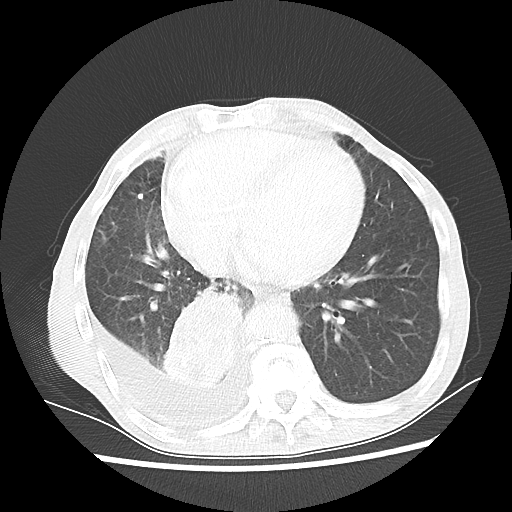
Chest CT, one axial slice; slice 22 of 60 in the series (ordered by position); reconstruction kernel LUNG; lung window (W 1500 / L -600 HU); 5 mm slice thickness; 512 × 512 image matrix. Male patient, age 76 years. From the clinical record (not read from this slice): clinical TNM (as recorded): T3 N3 M1a.
Annotated regions visible in this slice (rectangle marked by the reading radiologist):
- lung tumour (recorded histology: squamous cell carcinoma): bounding box <165,282,247,393> (left, top, right, bottom; pixels)